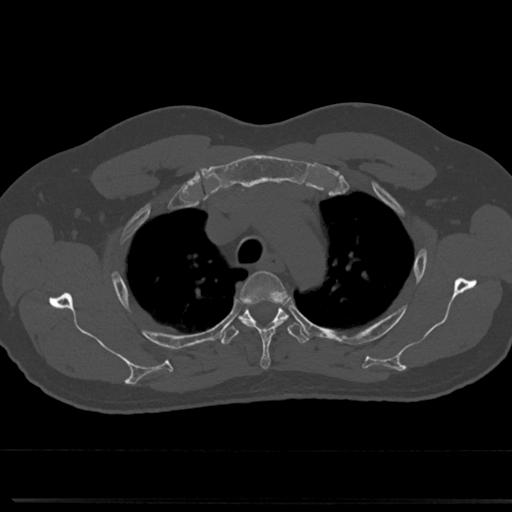
CT including the spine, one axial slice; position 570 of 817 along the scan axis; reconstruction kernel Br40s/3; 120 kVp; bone window (W 1800 / L 400 HU); 0.5 mm slice thickness; 512 × 512 image matrix. Male patient, age 61 years. Case-level facts recorded for this patient, not image findings: primary cancer: prostate.
Structures marked on this image (semi-automatic segmentation, software-assisted and operator-edited):
- T3 vertebra: bounding box (x1, y1, x2, y2) in pixels: (241, 270, 284, 369)
- T4 vertebra: (219, 300, 310, 345)